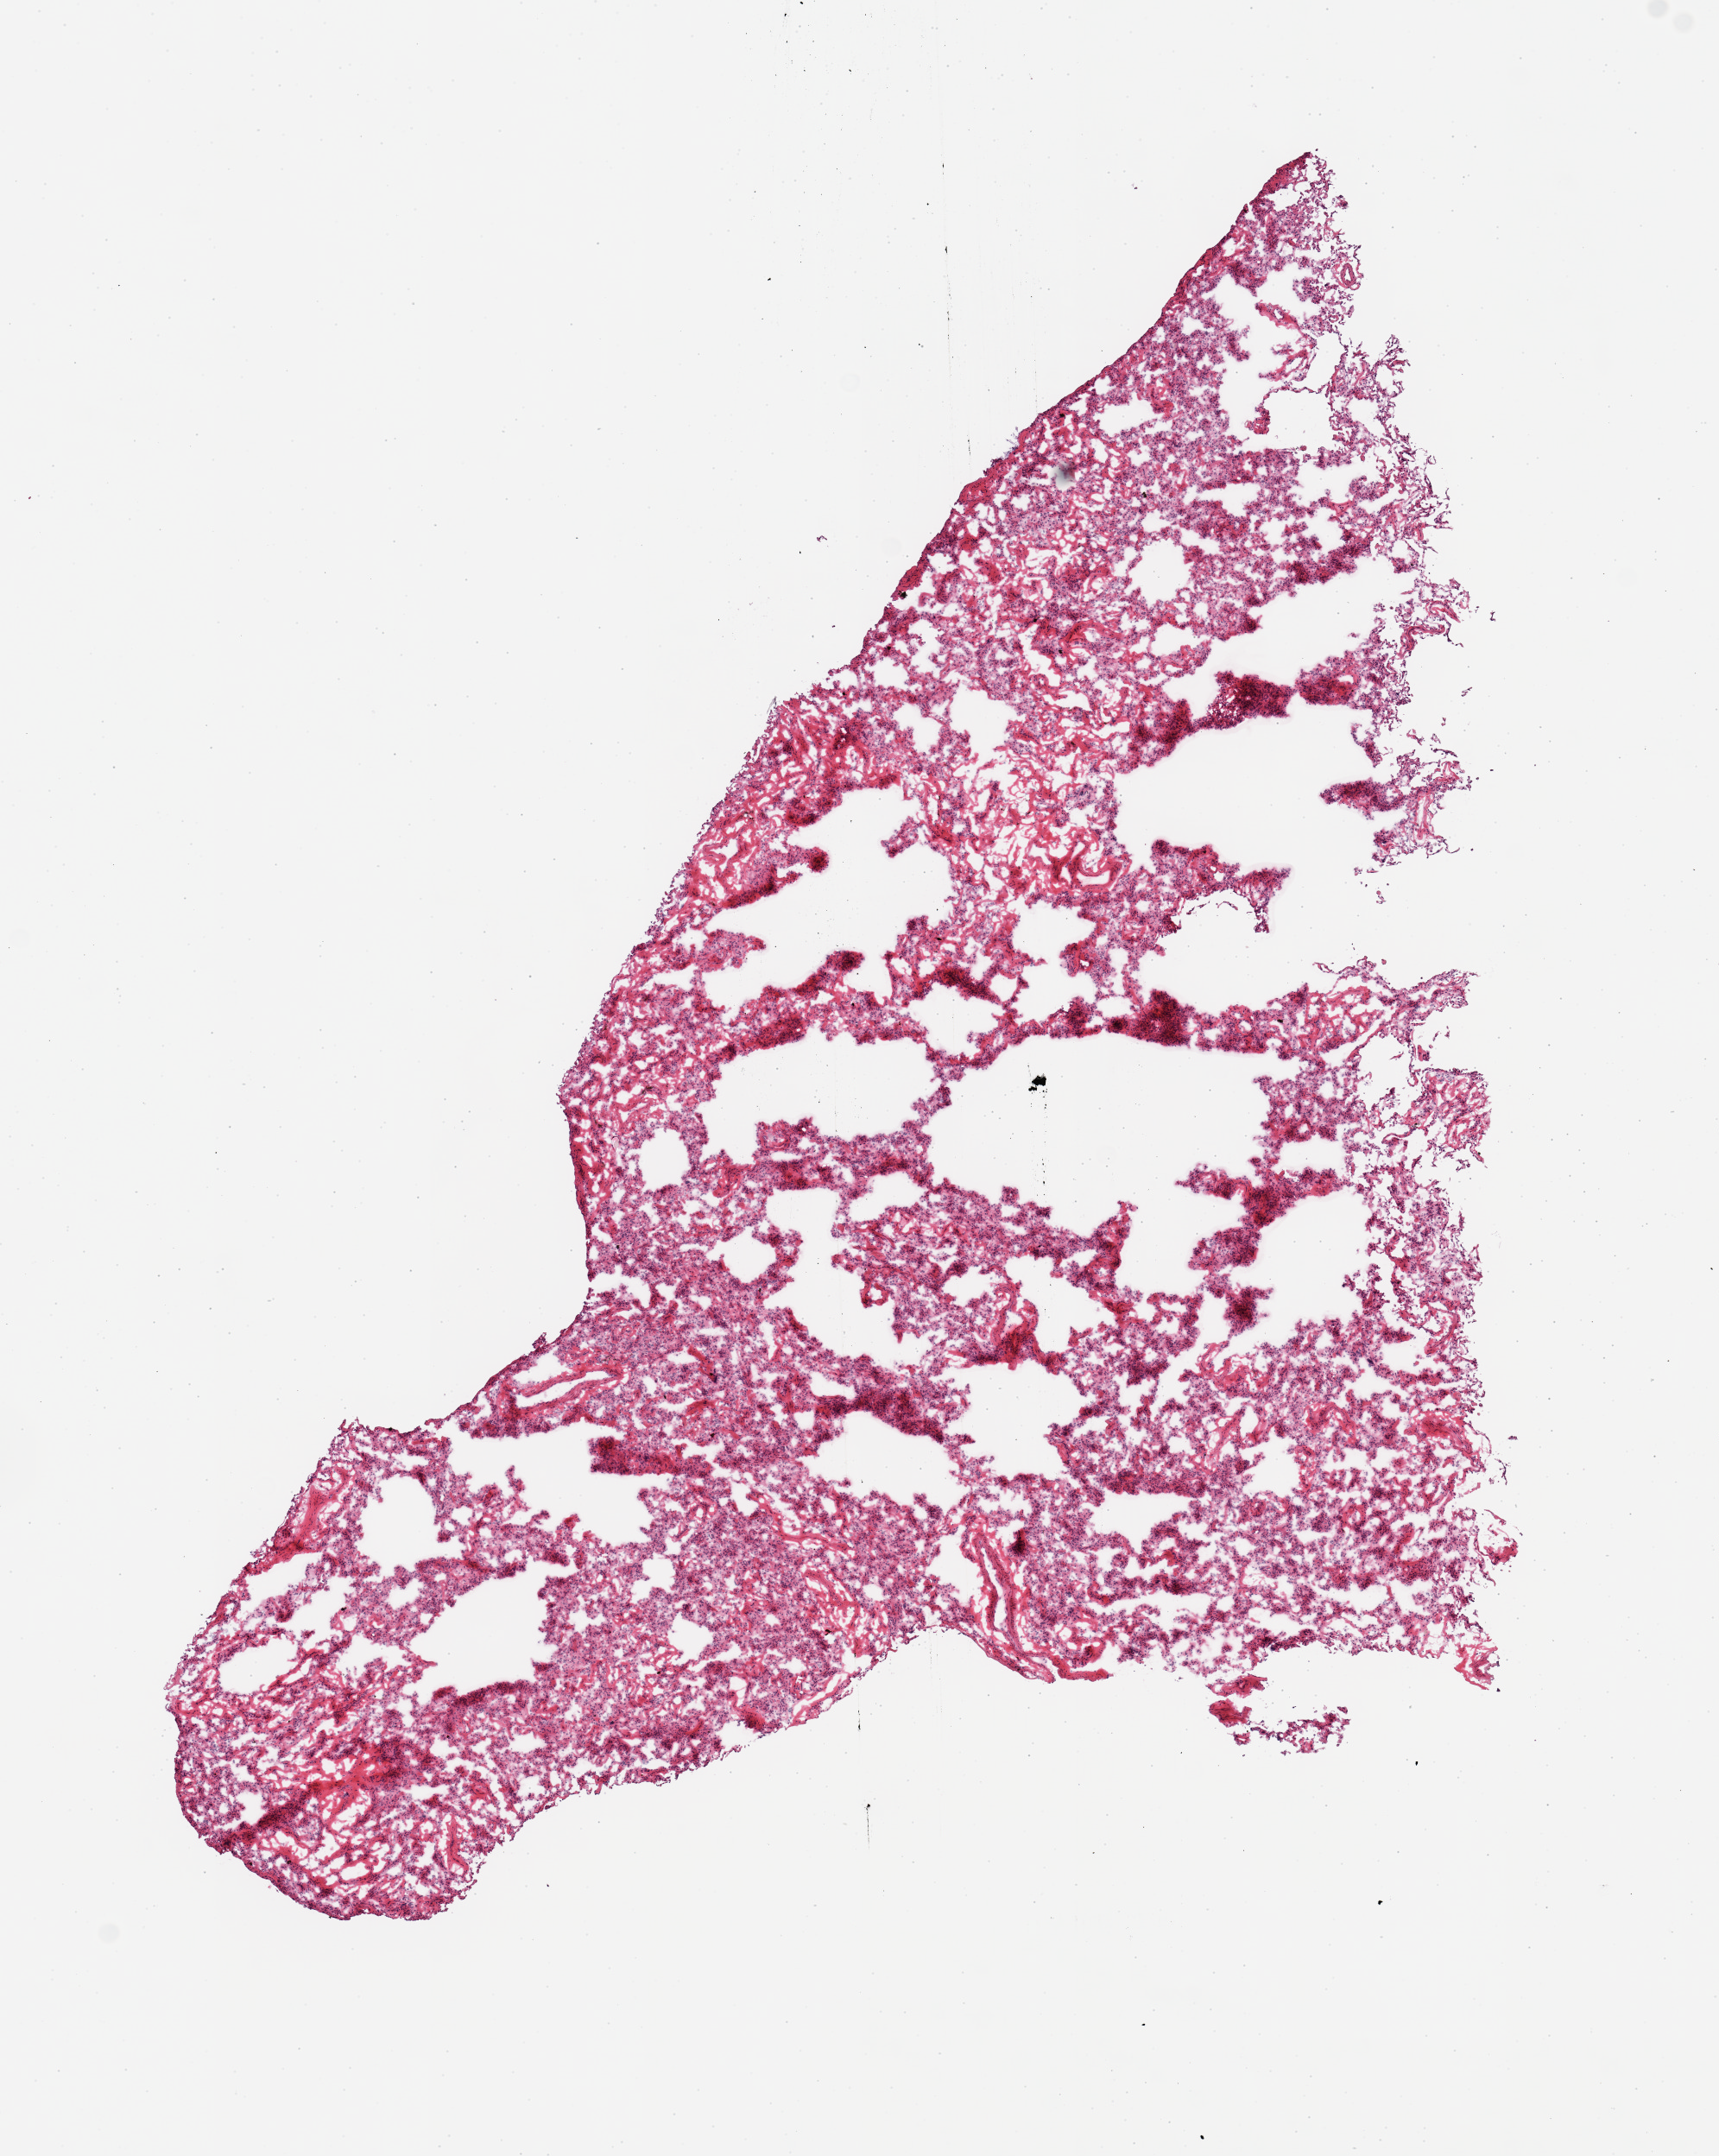
Digitized H&E-stained section, brightfield — whole scanned area (about 7.9 x 9.9 mm, slide scanned at 20x) shown as a low-resolution overview. Frozen section (dry ice). Sampled site (target tissue): lung. Donor tissue sample. Donor sex: male.
Reviewer comment on this tissue sample: 1 piece.